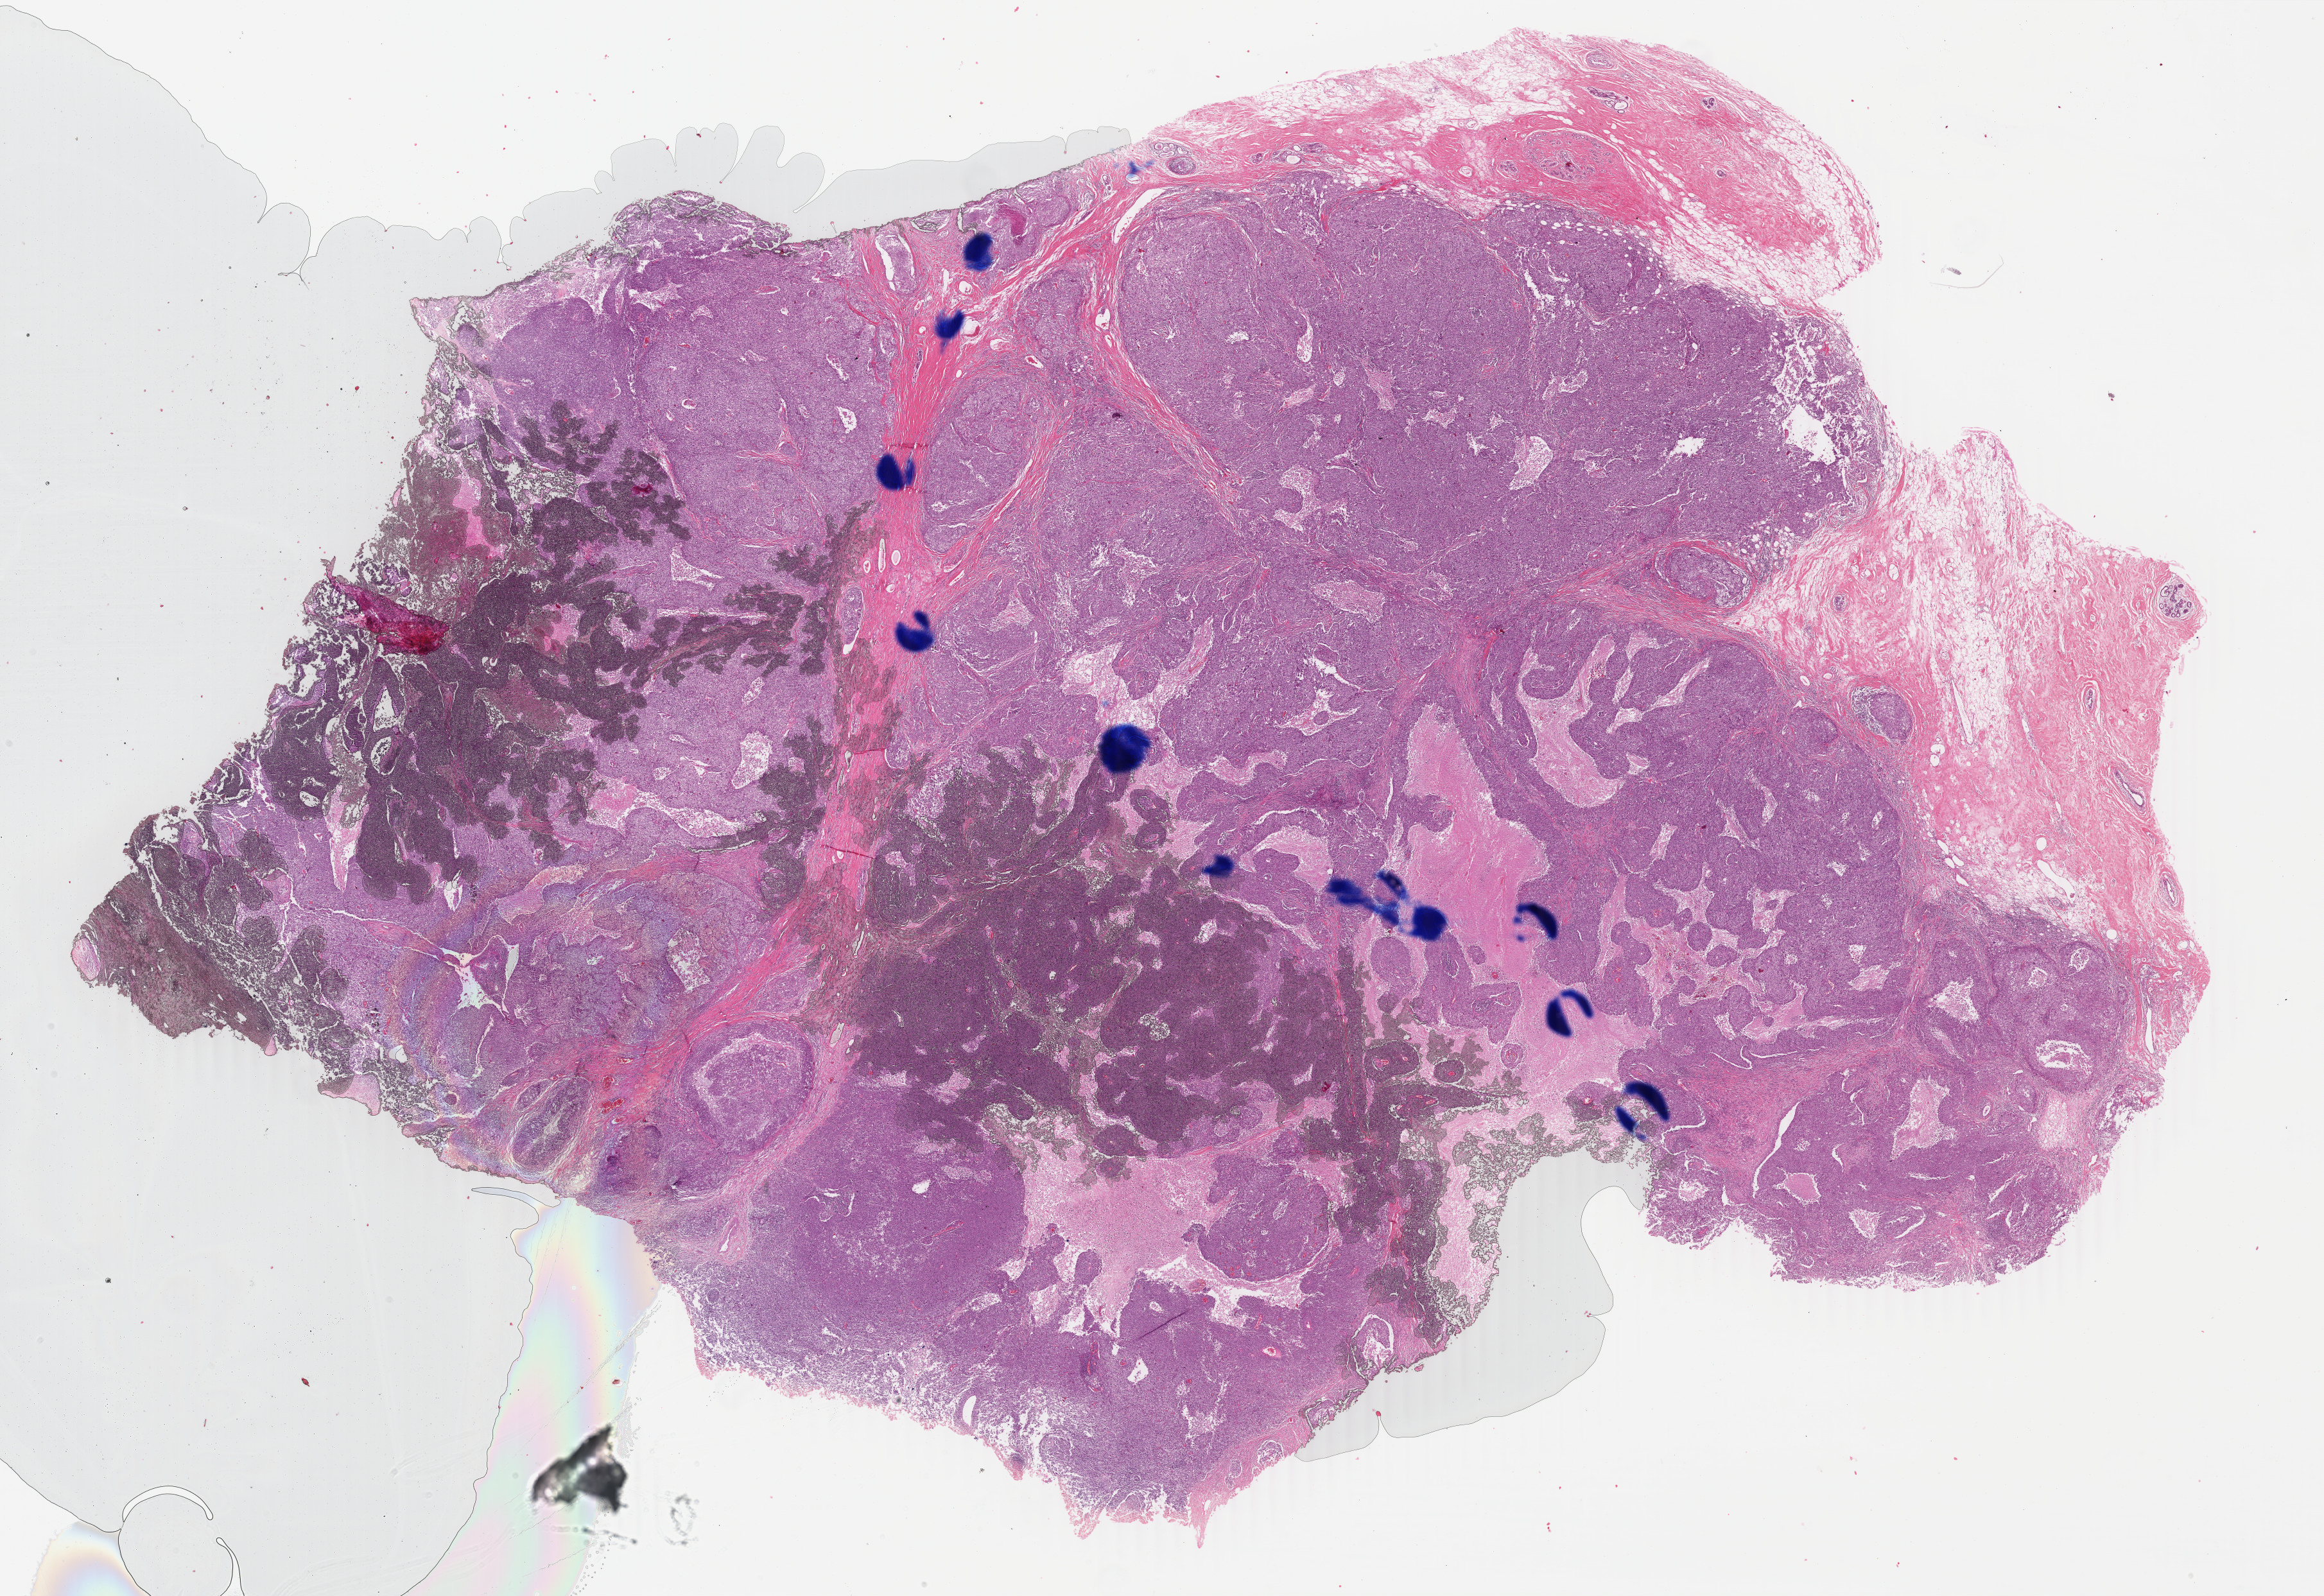
Whole-slide histology image, Hematoxylin and eosin (H&E) stained — shown as a low-resolution overview of the whole scanned area (about 28.8 x 19.8 mm). Formalin-fixed paraffin-embedded (FFPE) diagnostic section. Sample: primary tumour, breast. Female patient; age at initial diagnosis 40 years.
AJCC pathologic stage: IIIA (4th edition). Lymph nodes positive (case pathology): 1 of 26 examined. Diagnosis: Infiltrating duct carcinoma, NOS.